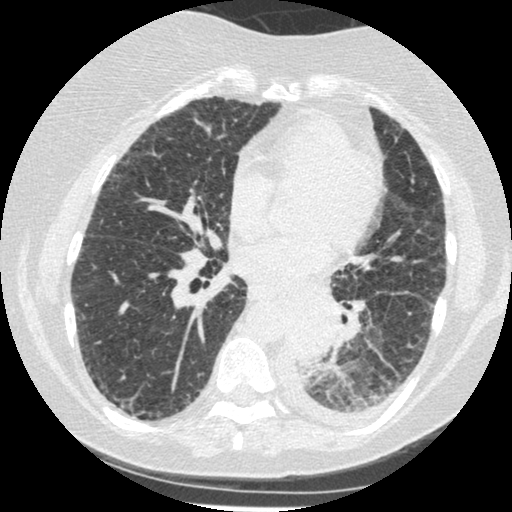
Low-dose screening chest CT, one axial slice; position 103 of 341 along the scan axis; reconstruction kernel STANDARD; 120 kVp; lung window (W 1500 / L -600 HU); 512 × 512 image matrix, field of view 310 × 310 mm.
Outlined on this slice (expert manual segmentation):
- lesion 1 (tumor, lower lobe of left lung): bounding box [x1, y1, x2, y2] px = [286, 305, 338, 364]